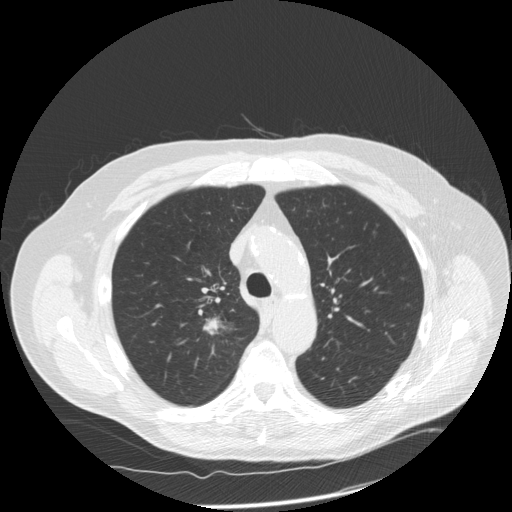
Low-dose screening chest CT, axial slice; third screening round (two years after baseline); lung window (W 1500 / L -600 HU); 2.5 mm slice thickness; slice 48 of 166 in the series; 512 × 512 image matrix, field of view 390 × 390 mm. Male participant, aged 69 years at enrolment.
• Lesion marked by an expert reader, bounding box (x1, y1, x2, y2) in pixels: (182, 305, 242, 353).
• The exam's reader record, not a measurement of the box and not confirmed to be the same lesion: non-calcified nodule or mass ≥4 mm, right upper lobe, 18 × 17 mm, spiculated (stellate) margins, soft tissue attenuation, pre-existing on the prior screen: no.
• Official screen result: positive, other.
• Later outcome: lung cancer diagnosed 13 days after this screen — squamous cell carcinoma, NOS, right upper lobe, poorly differentiated (G3), stage IA (AJCC 6th edition), 22 mm at pathology.